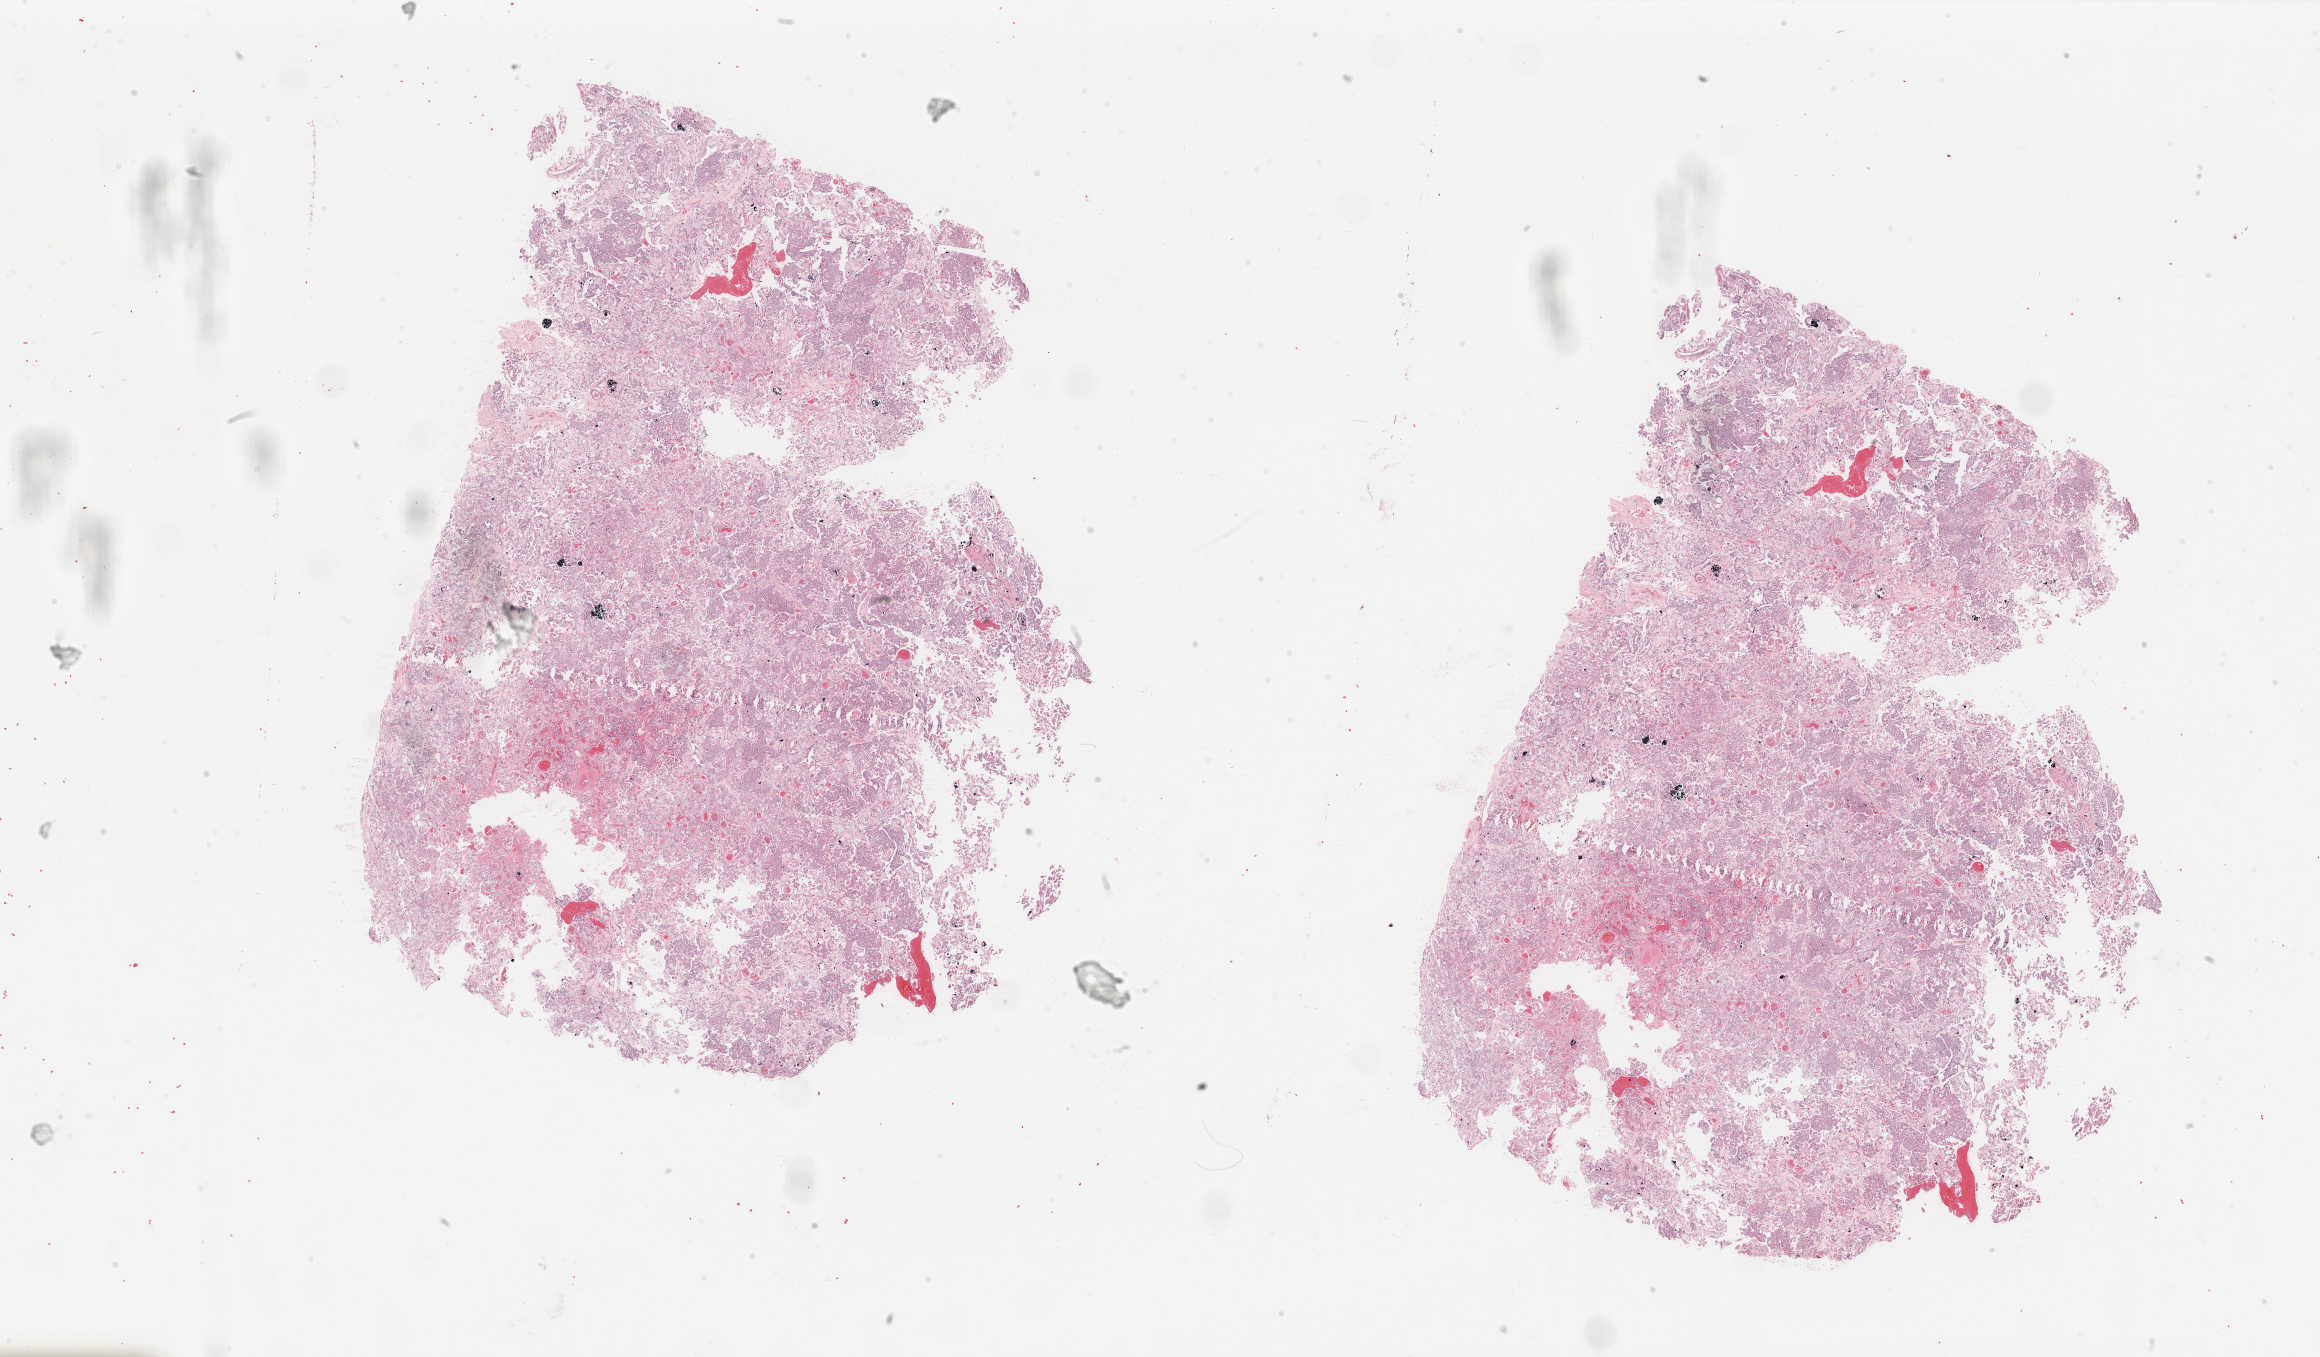
Whole-slide histology image, H&E, shown as a low-resolution overview of the whole scanned area (about 36.7 x 21.5 mm), FFPE section, kidney, primary tumour sample. Patient: male, age at initial diagnosis 48 years.
* histologic diagnosis: Renal cell carcinoma, chromophobe type
* AJCC pathologic stage: III (7th edition)